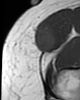
MRI of an extremity soft-tissue mass, one axial slice. Position 13 of 46 along the scan axis. MR volume resampled by the dataset authors to the PET/CT grid (not the native acquisition matrix). 3.27 mm slice thickness. 80 × 100 image matrix, field of view 78 × 98 mm. Female patient. From the clinical record (not read from this slice): histological type: synovial sarcoma; grade: intermediate; site of the primary tumour: right thigh.
Structures marked on this image (expert contour drawn on MRI and transferred to this co-registered scan by the dataset authors):
- gross tumour volume including surrounding oedema: bounding box (x1, y1, x2, y2) in pixels: (35, 26, 56, 52)
- gross tumour volume (mass): (35, 26, 56, 52)